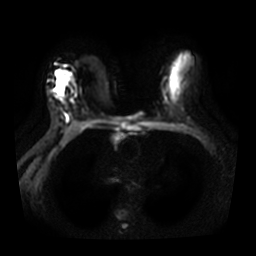
Breast MRI, one axial slice; position 19 of 31 along the scan axis; diffusion-weighted series; image 2 of 4 stored at this slice position (different b-values; order by instance number); 3 T; 5 mm slice thickness; 256 × 256 image matrix. Female patient.
Structures marked on this image (outlined manually by an expert reader):
- tumour on diffusion-weighted imaging: bounding box (x1, y1, x2, y2) in pixels: (58, 75, 64, 93)